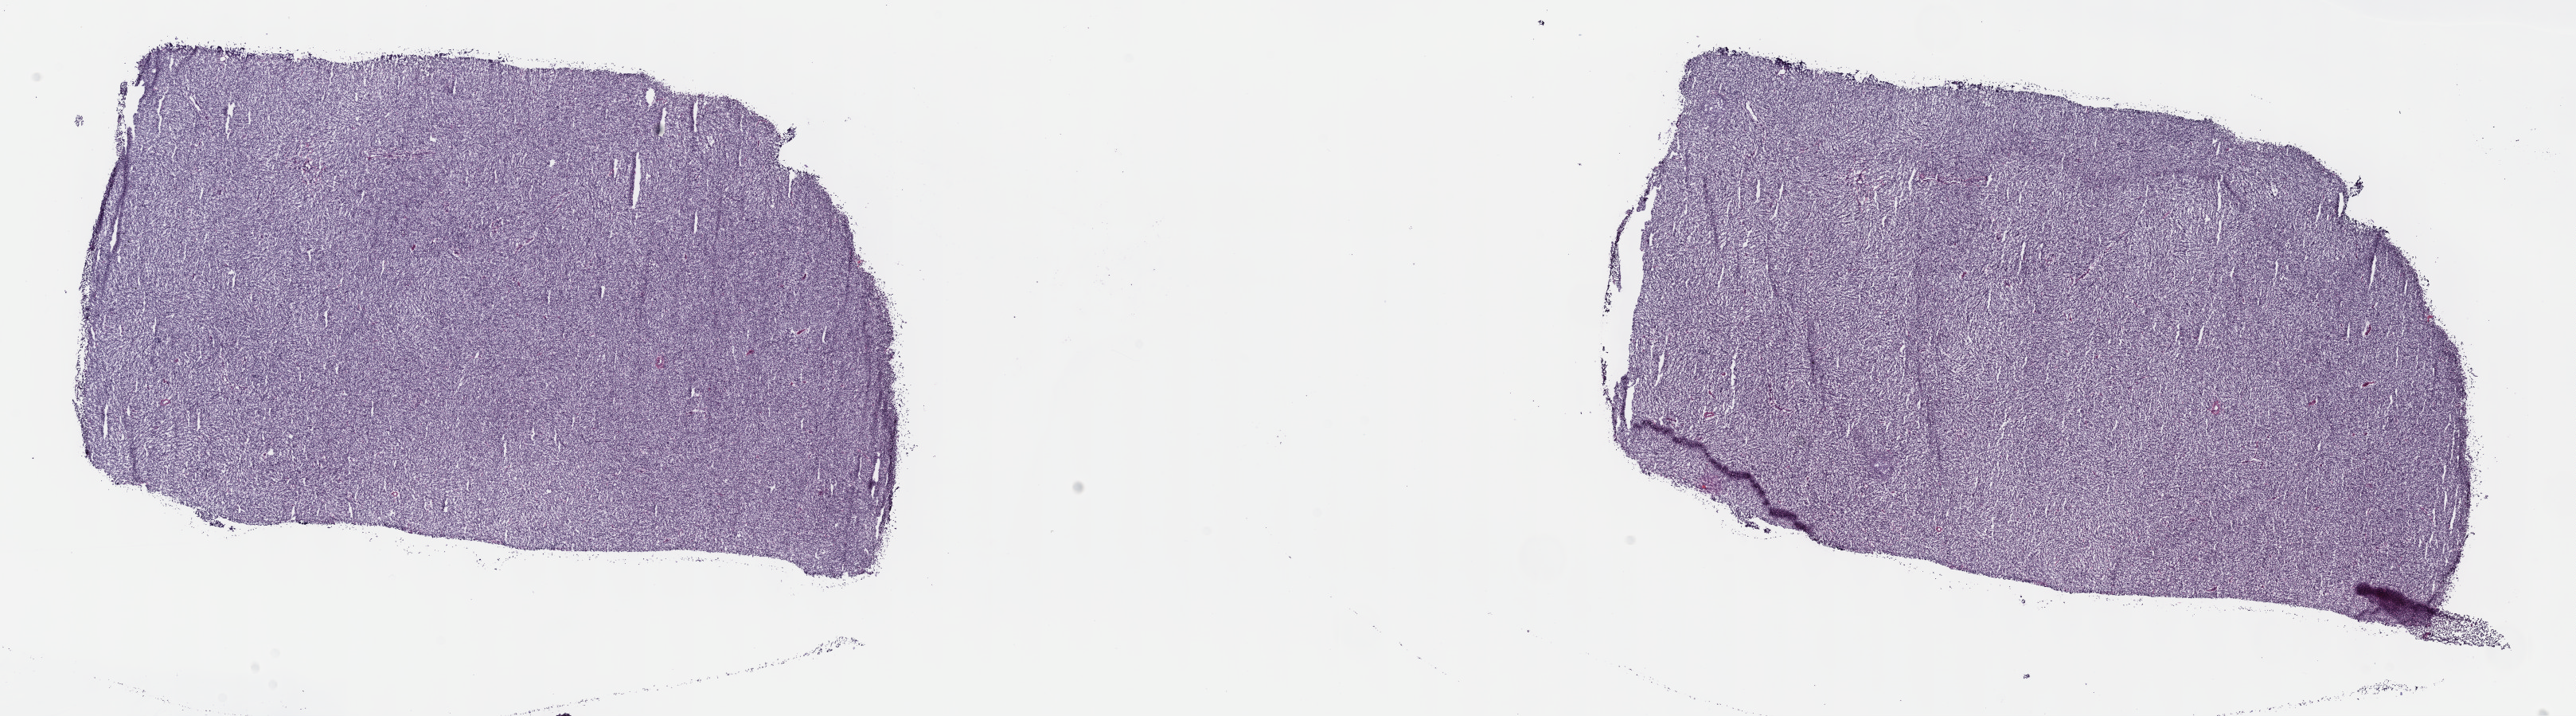
Digitized H&E tissue section (whole slide), shown as a low-resolution overview of the whole scanned area (about 26.2 x 7.3 mm, slide scanned at 40x); frozen section from the top of the tissue portion; sample: primary tumour, lymphoid tissue. Male, age 37 years at initial diagnosis. Composition of this section per pathologist review: tumour cells 95%, tumour nuclei 95%, normal cells 0%, stromal cells 5%, necrosis 0%. Inflammatory infiltration, as recorded: lymphocyte infiltration 90%, monocyte infiltration 5%, neutrophil infiltration 0%.
Diagnosis: Diffuse large B-cell lymphoma, NOS (lymph nodes of inguinal region or leg).